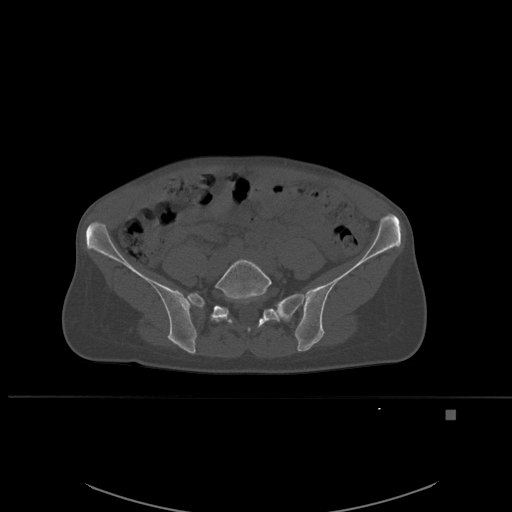
CT including the spine, one axial slice. Position 166 of 537 along the scan axis. Bone window (W 1800 / L 400 HU). 1.5 mm slice thickness. 512 × 512 image matrix, field of view 440 × 440 mm. Patient: female, 45 years. From the clinical record (not read from this slice): primary cancer: lung.
Structures marked on this image (semi-automatically segmented with operator editing):
- L5 vertebra: bounding box [x1, y1, x2, y2] px = [210, 258, 272, 332]